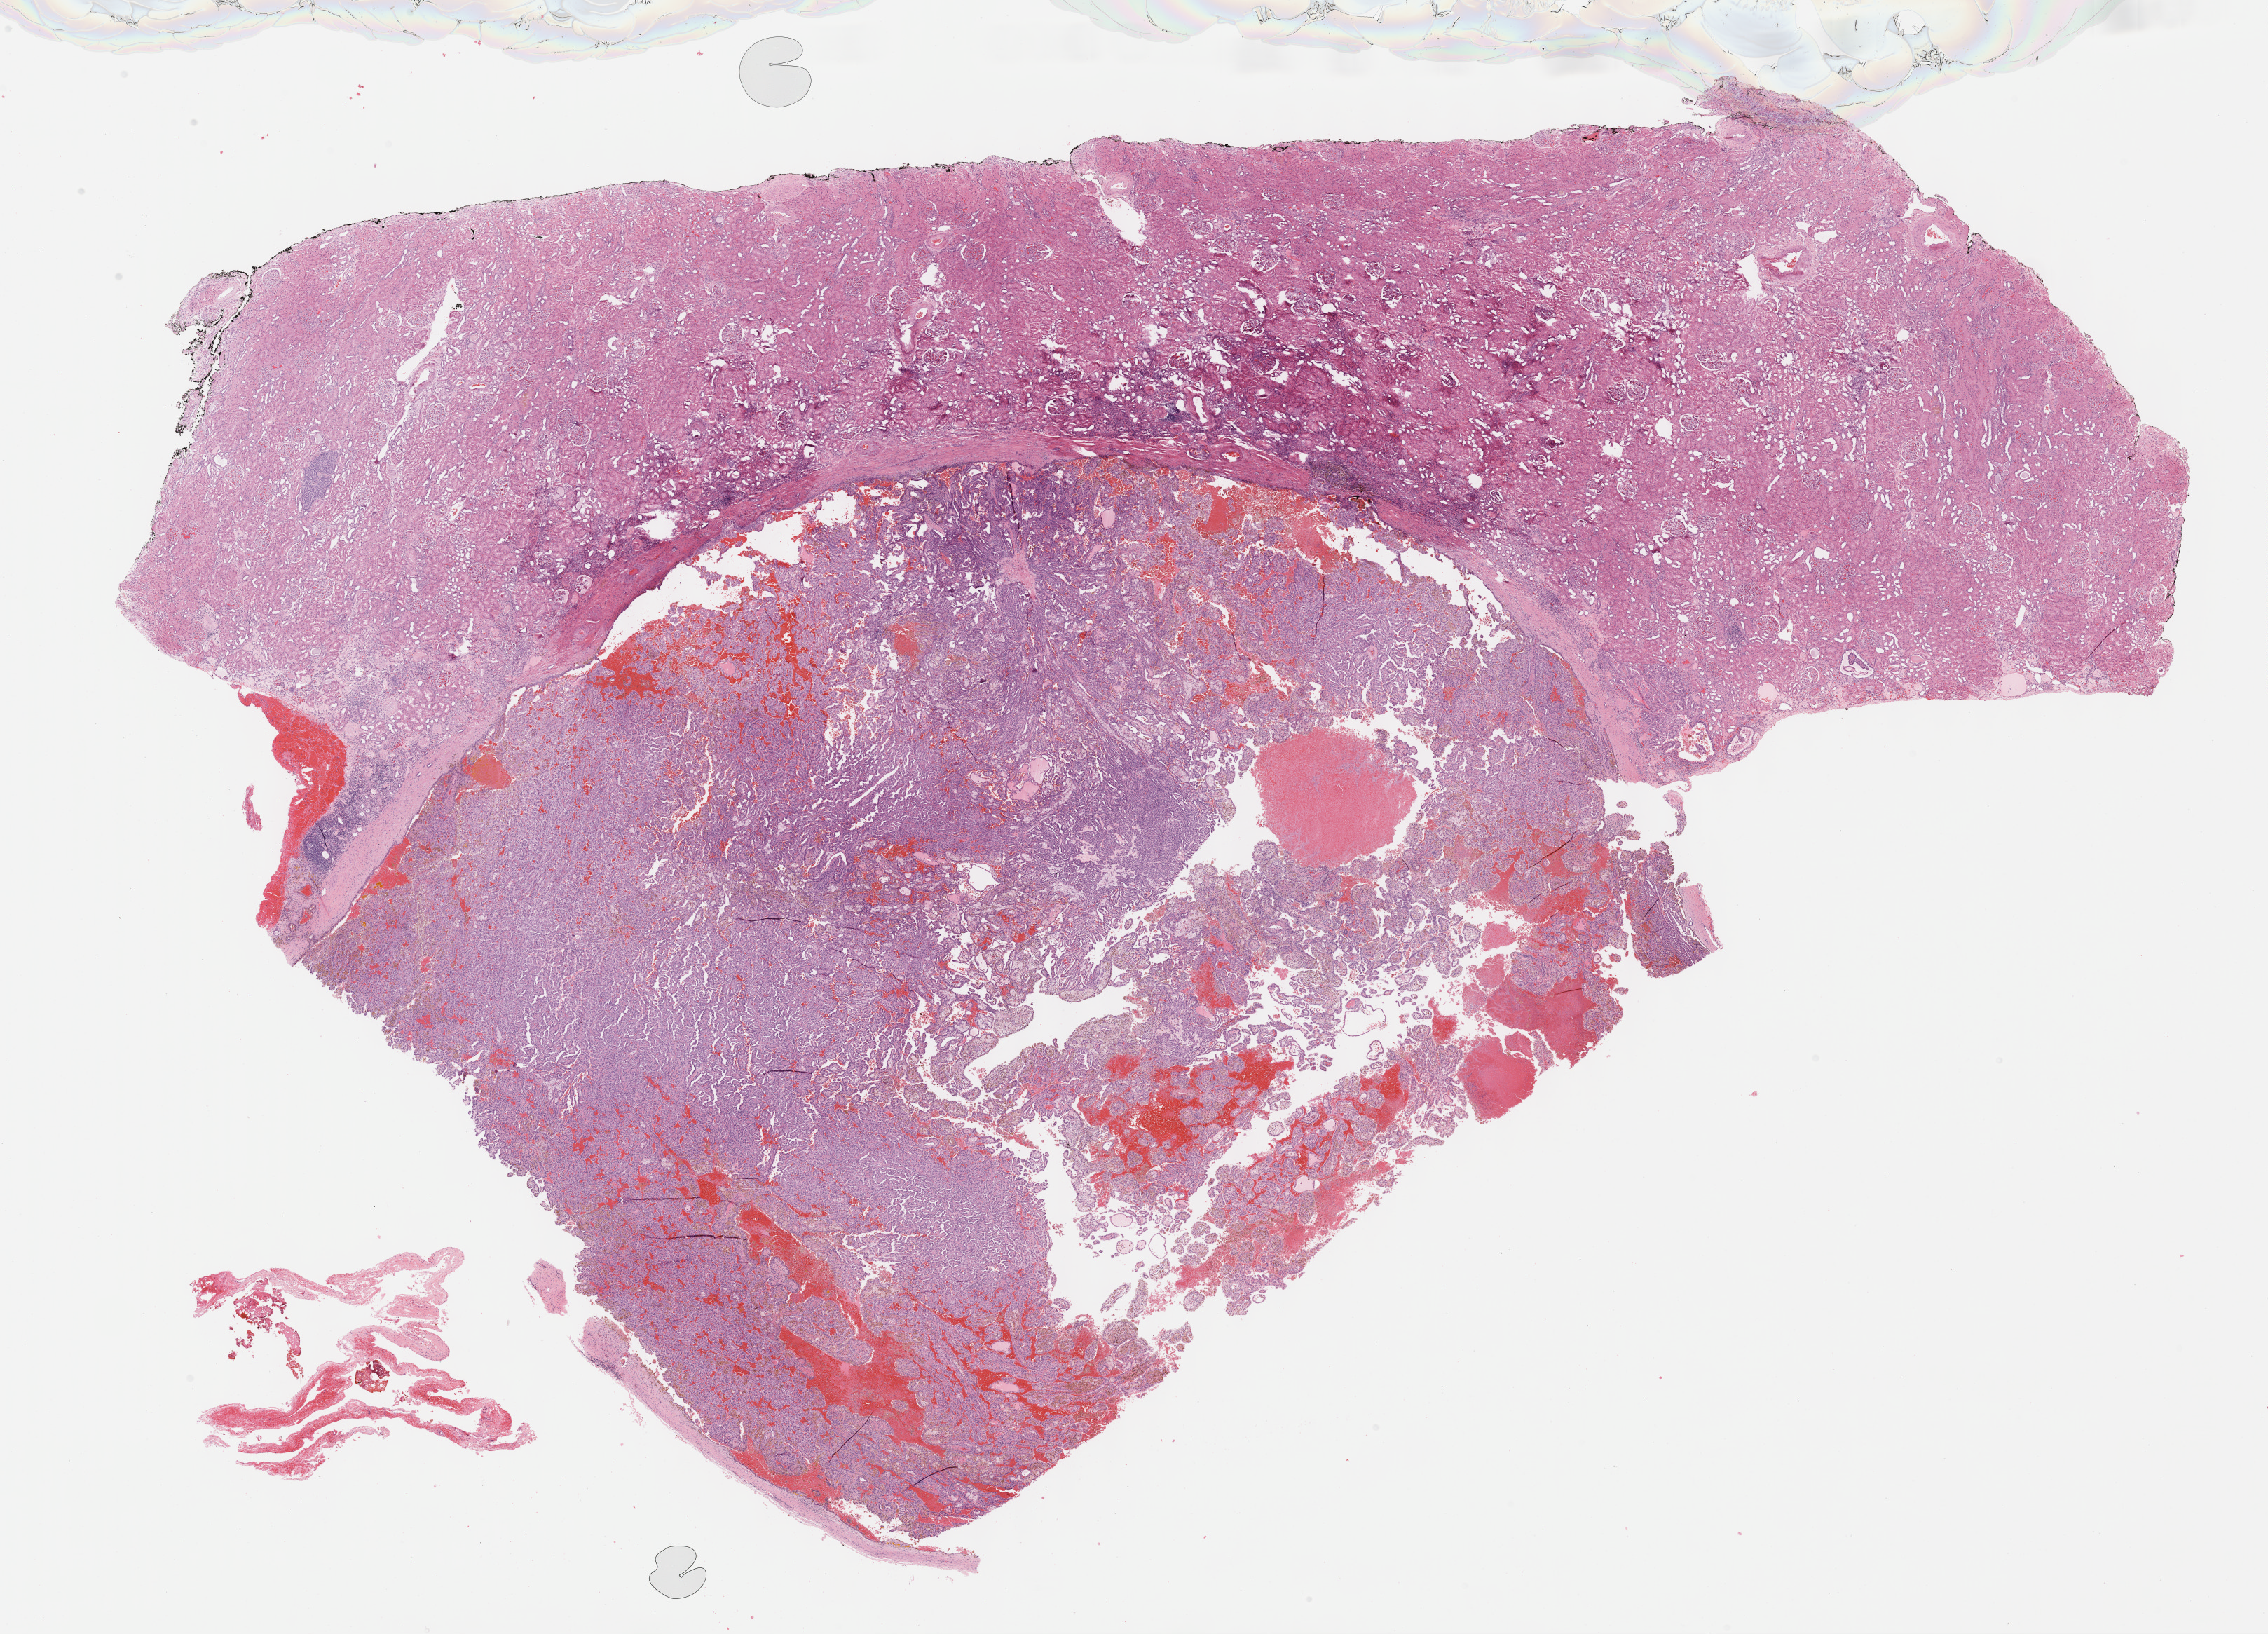
Digitized Hematoxylin and eosin (H&E) stained tissue section (whole slide) — a low-resolution overview of the entire scanned area, about 26.2 x 18.9 mm. Formalin-fixed paraffin-embedded (FFPE) diagnostic section. Sample: primary tumour, kidney. Patient: male, age at initial diagnosis 71 years.
Laterality: left. Diagnosis: Papillary adenocarcinoma, NOS. AJCC pathologic stage: I (6th edition).